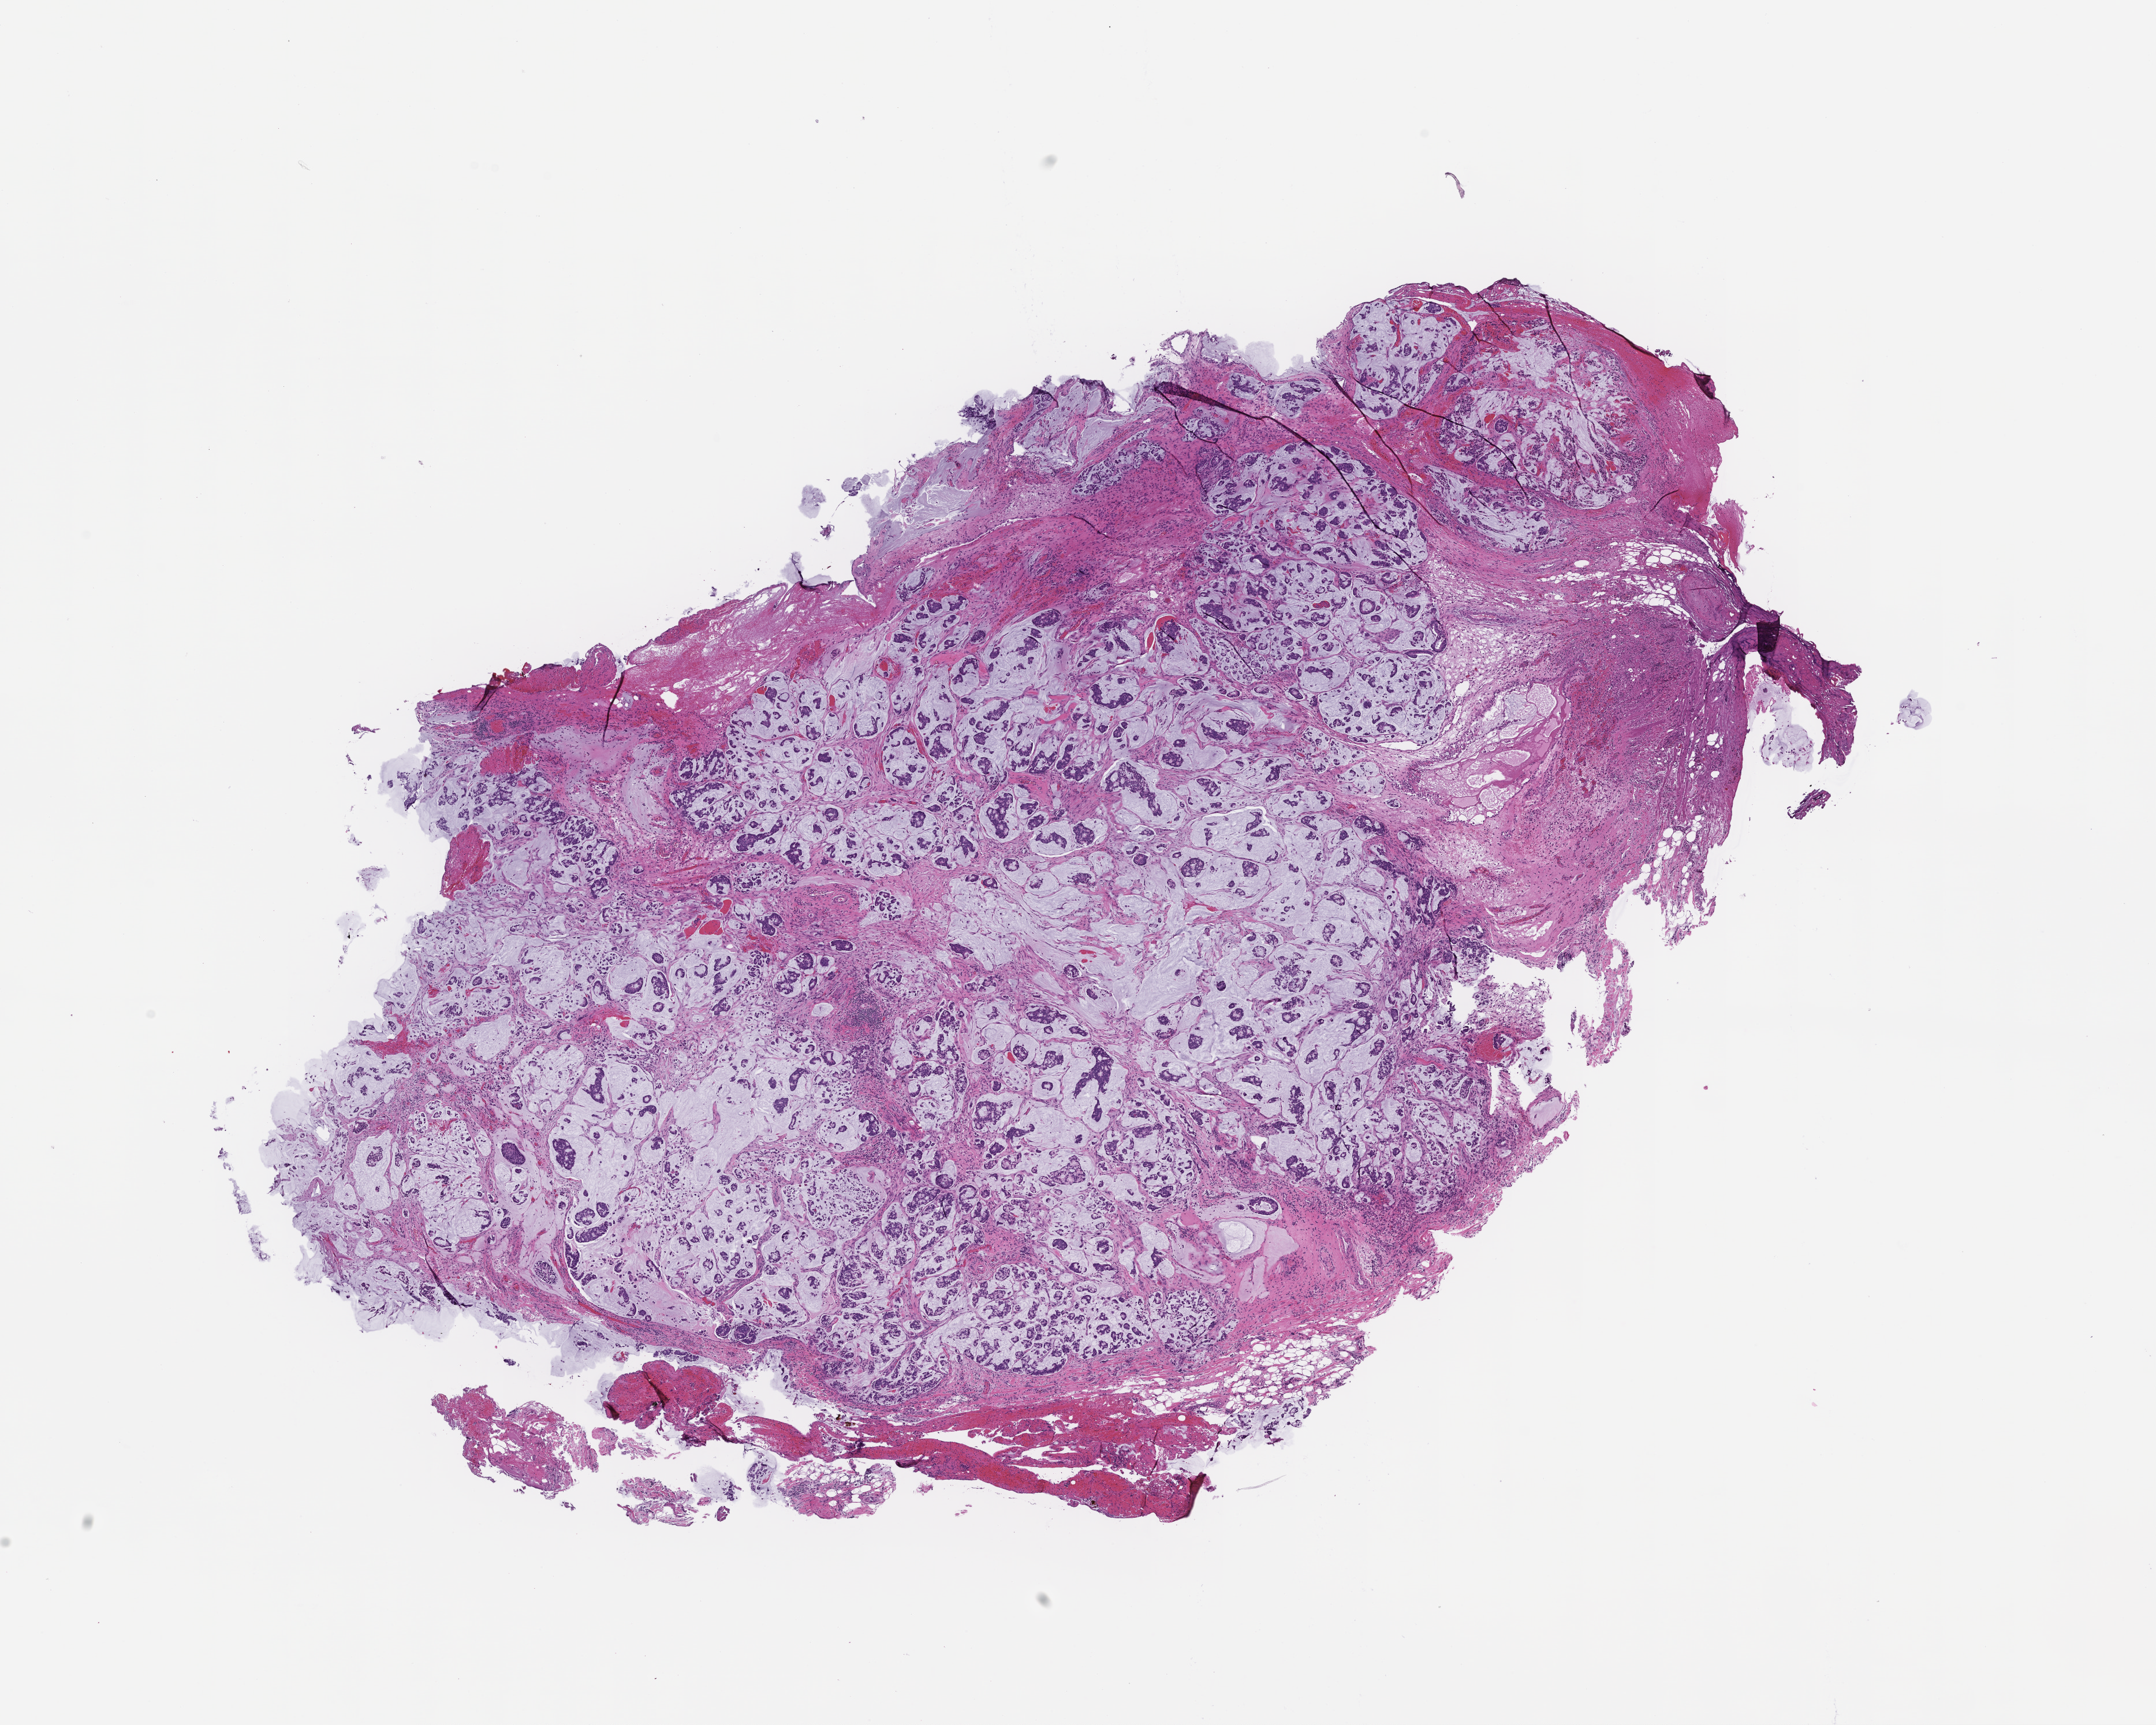
Digitized haematoxylin and eosin-stained section — shown as a low-resolution overview of the whole scanned area (about 15.1 x 12.1 mm), FFPE section, site: colon, collected at disease progression. Patient: male.
Patient diagnosis: Colorectal Carcinoma.